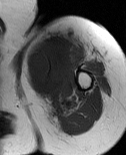
MRI of an extremity soft-tissue mass, one axial slice; slice 57 of 86 in the series (ordered by position); MR volume resampled by the dataset authors to the PET/CT grid (not the native acquisition matrix); 3.27 mm slice thickness; 126 × 155 image matrix, field of view 123 × 151 mm. Female patient. From the clinical record (not read from this slice): histological type: pleiomorphic leiomyosarcoma; grade: high; site of the primary tumour: left biceps.
Outlined on this slice (expert contour drawn on MRI and transferred to this co-registered scan by the dataset authors):
- gross tumour volume including surrounding oedema: bounding box (x1, y1, x2, y2) in pixels: (27, 38, 76, 112)
- gross tumour volume (mass): (25, 38, 75, 96)